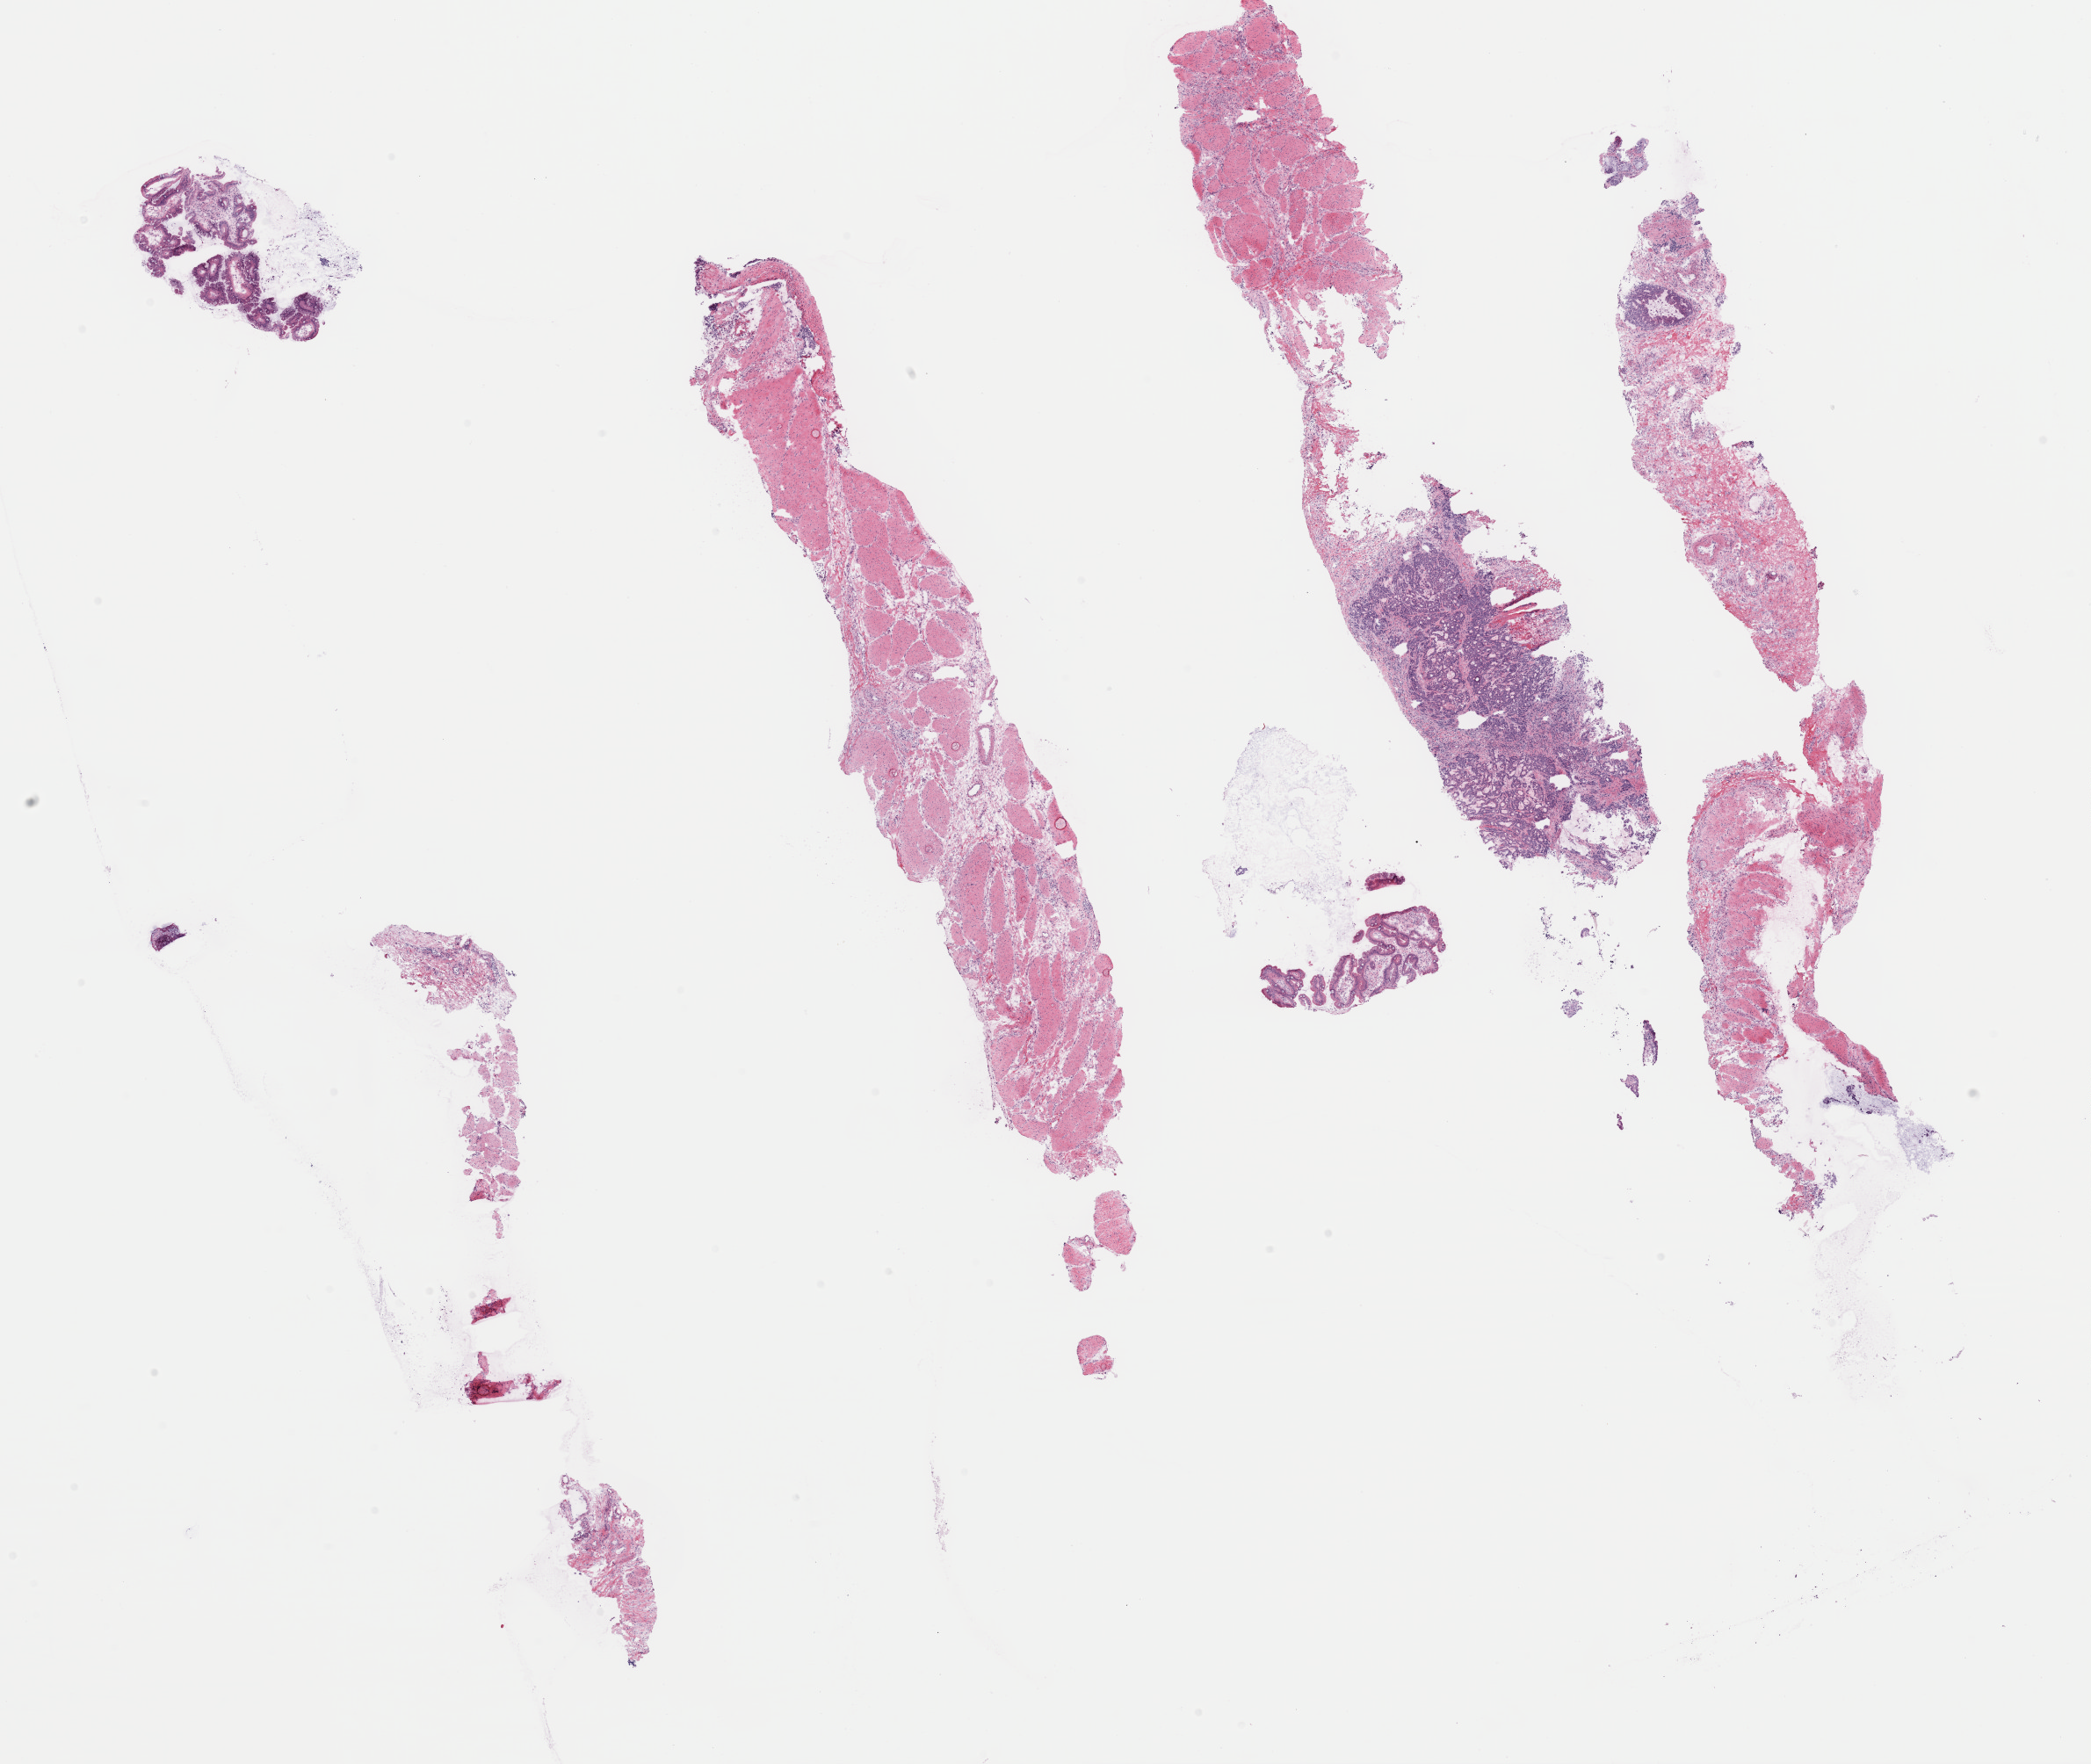
Whole-slide histology image, H&E, a low-resolution overview of the entire scanned area, about 18.8 x 15.9 mm (slide scanned at 40x); frozen section from the top of the tissue portion; stomach, primary tumour sample. Female, age 86 years at initial diagnosis. Histologic grade: G3 (poorly differentiated). Slide review estimates, as recorded: tumour cells 20%, tumour nuclei 80%, normal cells 60%, stromal cells 0%, necrosis 20%. Infiltration values recorded for this section: lymphocyte infiltration 0%, monocyte infiltration 0%, neutrophil infiltration 0%.
• AJCC pathologic stage: IIIA
• histologic diagnosis: Tubular adenocarcinoma (gastric antrum)
• TNM: T3 N2 M0